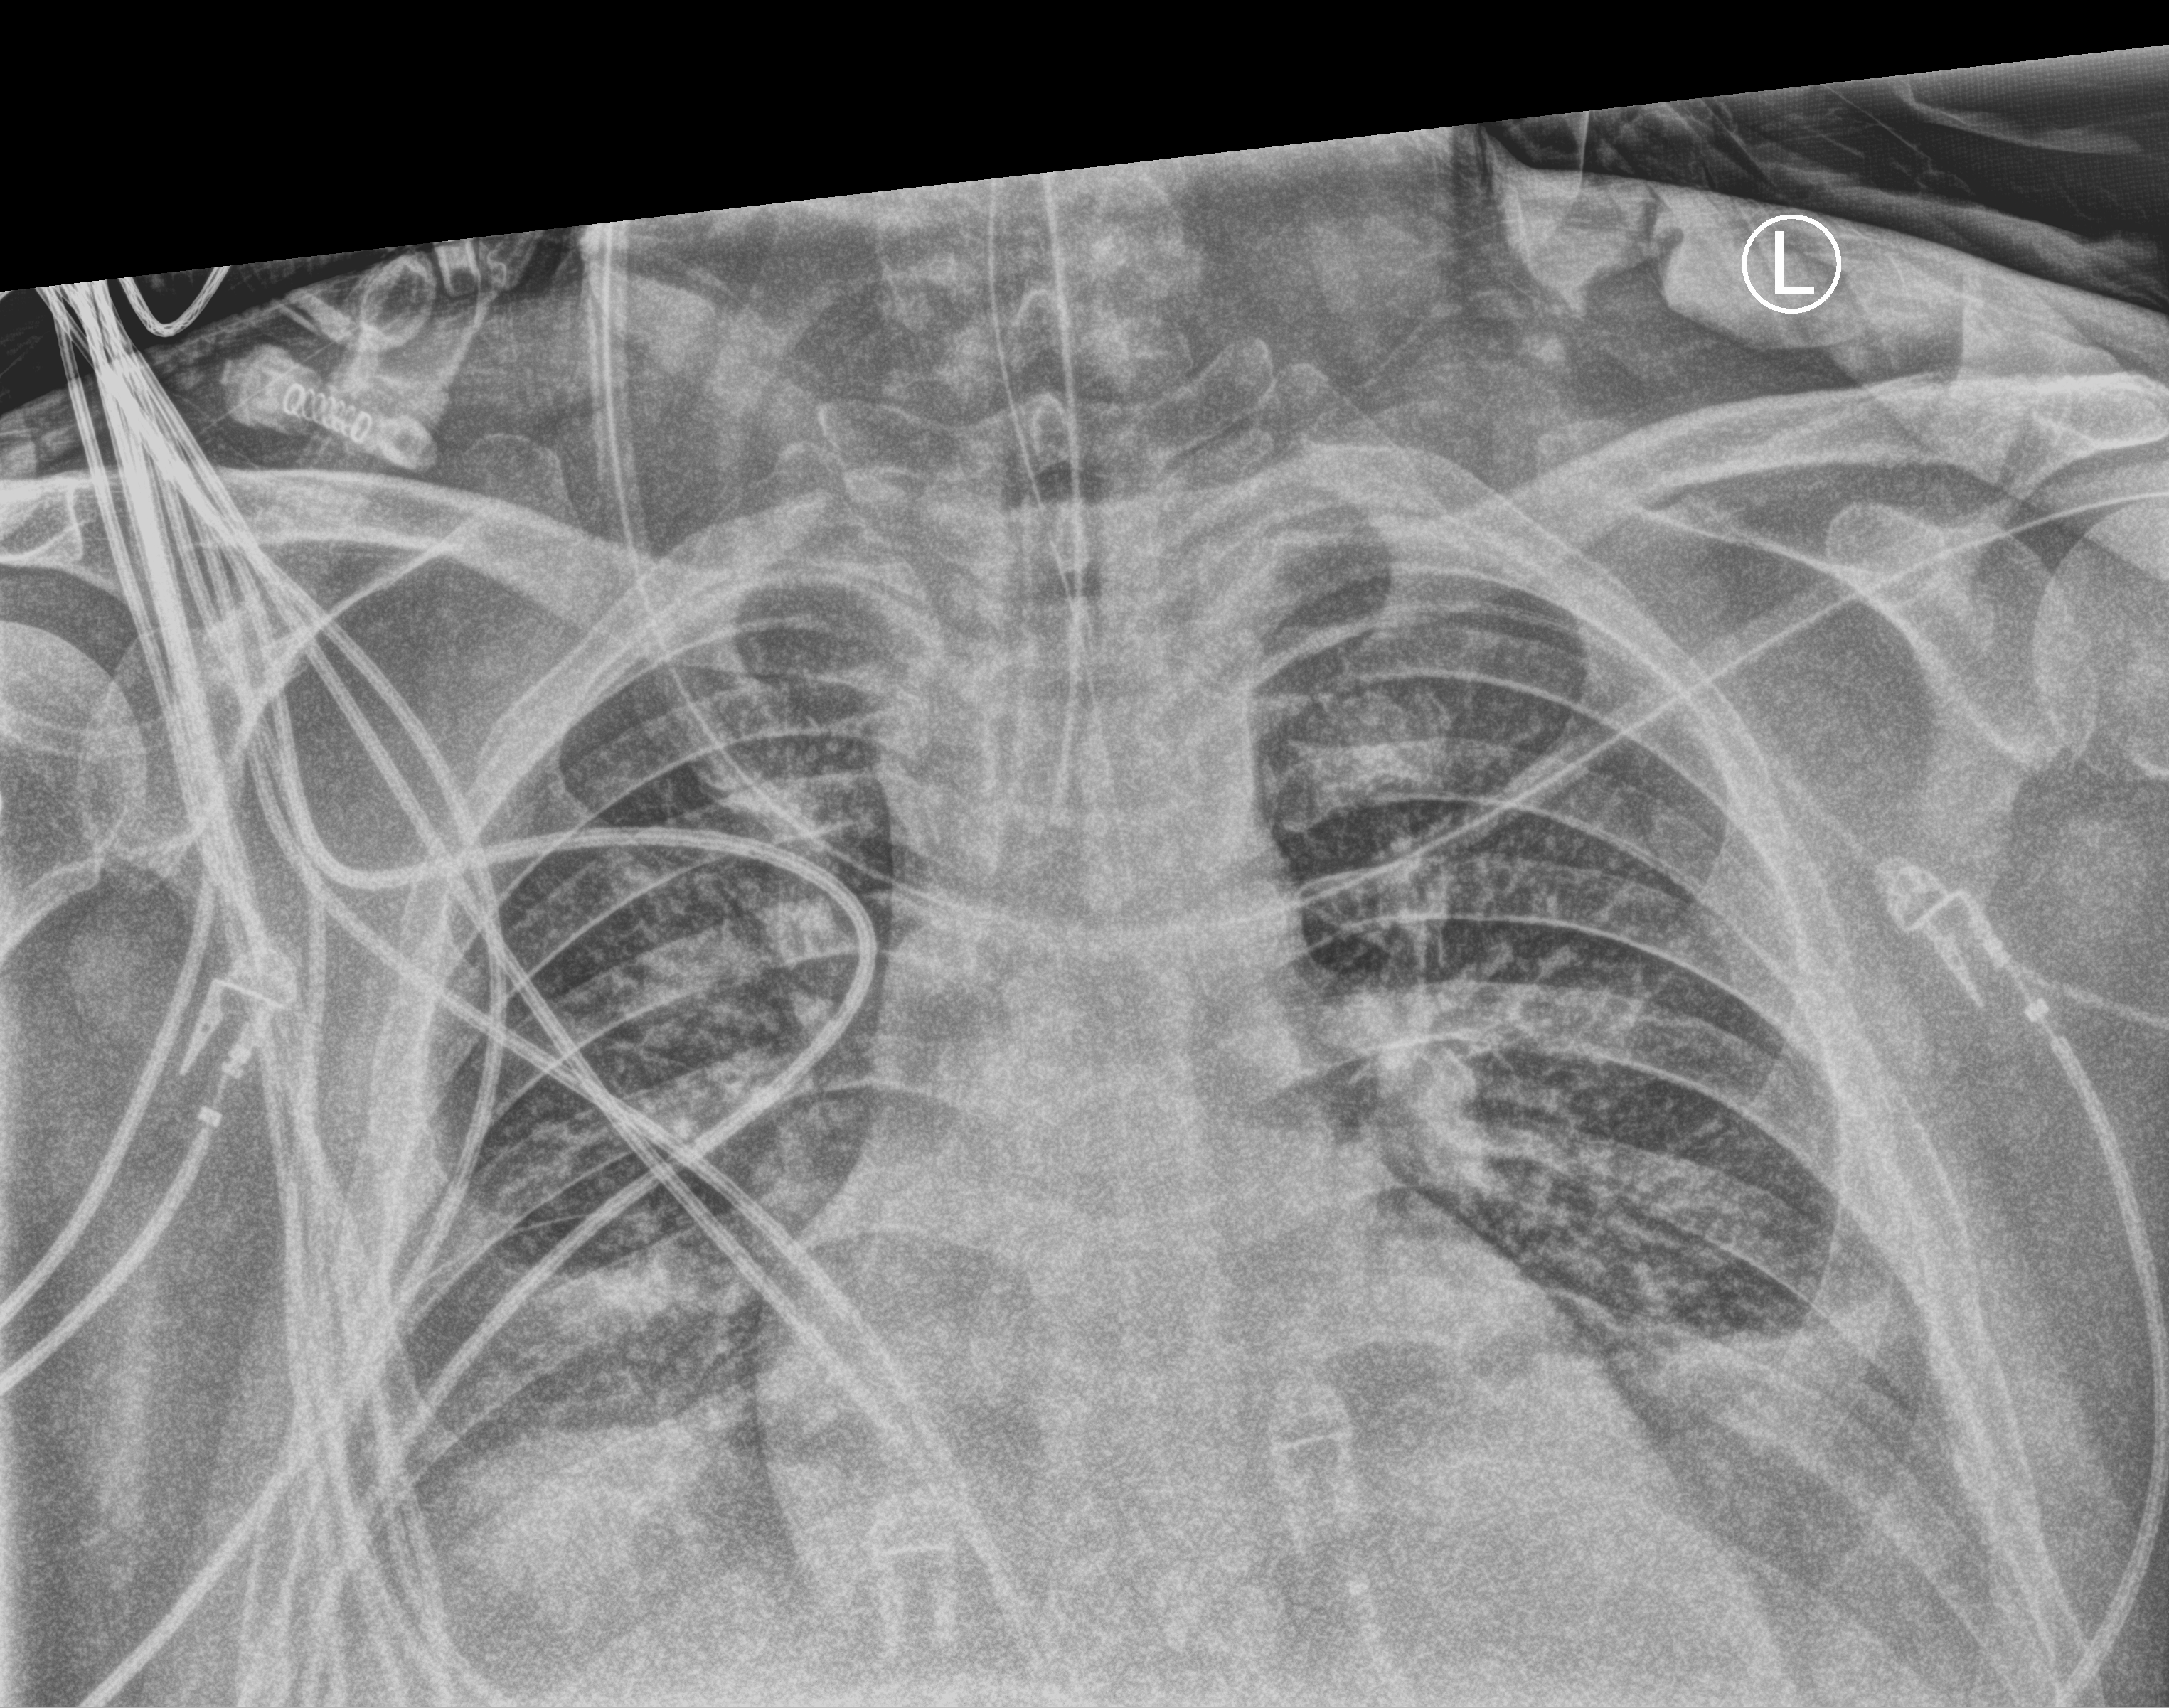
Bedside chest radiograph (computed radiography); anteroposterior (AP) projection. Patient hospitalised with COVID-19; male, aged 18–59 years.
Hospital-stay facts (about this admission, not read from this image; timing relative to this image not recorded): mechanically ventilated during this hospital stay: yes; admitted to intensive care during this hospital stay: yes.